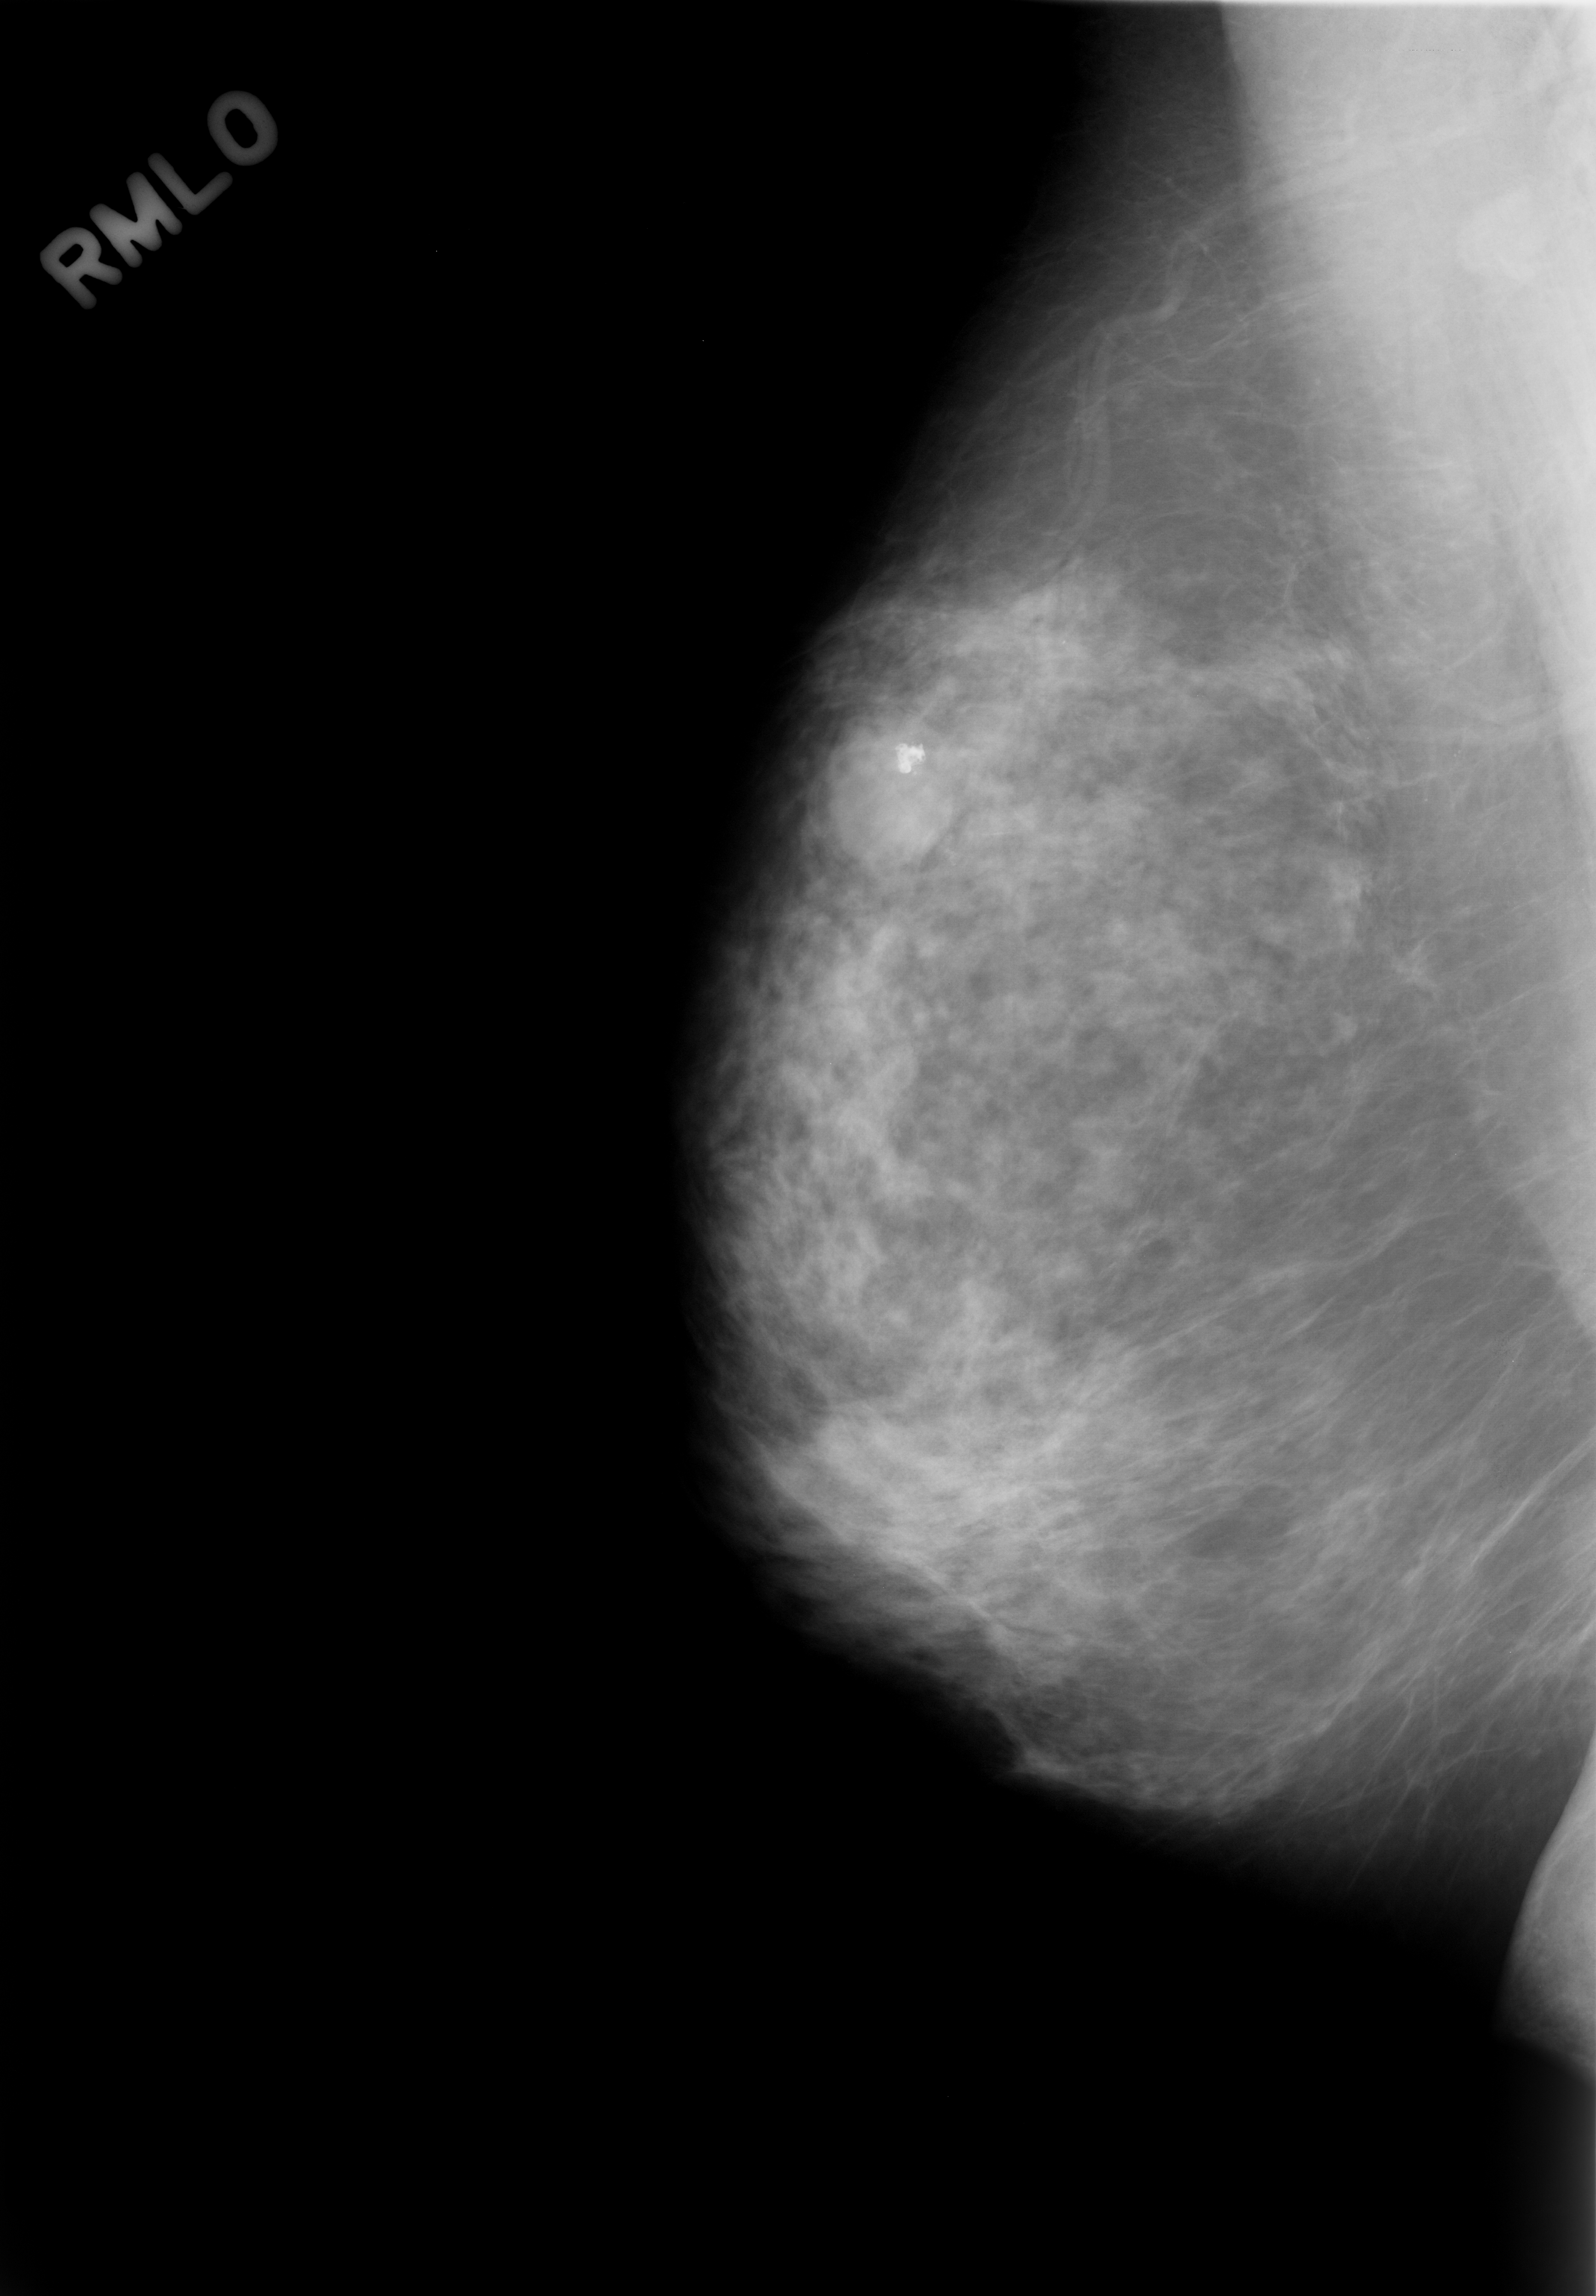
Scanned film-screen mammogram. Right breast. Mediolateral oblique (MLO) view. BI-RADS breast density category 2 (scale 1–4). 1596 × 2296 image matrix.
Expert-marked regions of interest on this film, with their recorded descriptors:
- mass, shape oval, margins microlobulated; BI-RADS assessment category 4; pathology (as recorded): benign: bounding box <851,726,960,866> (left, top, right, bottom; pixels)